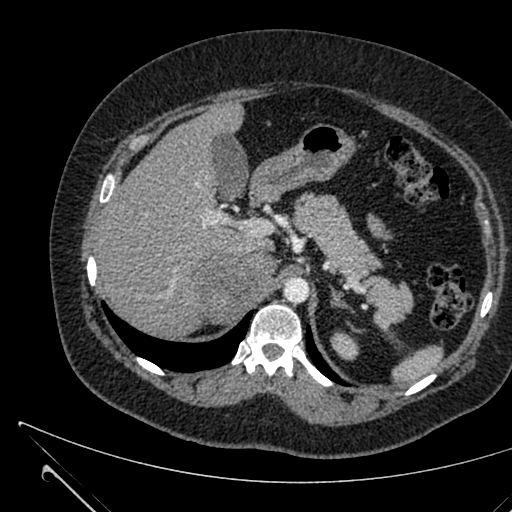
Contrast-enhanced abdominal CT, one axial slice; slice 459 of 731 in the series (ordered by position); 120 kVp; intravenous contrast given; soft-tissue window (W 400 / L 40 HU); 1 mm slice thickness; 512 × 512 image matrix, field of view 376 × 376 mm. Patient: female, 36 years. Case-level facts recorded for this patient, not image findings: diagnosis: adrenocortical carcinoma; tumour side: right adrenal; tumour size at pathology: 10 cm; Ki-67 index: 20 %.
Annotated regions visible in this slice (semi-automatic segmentation, software-assisted and operator-edited):
- mass: bounding box [x1, y1, x2, y2] px = [199, 253, 272, 322]